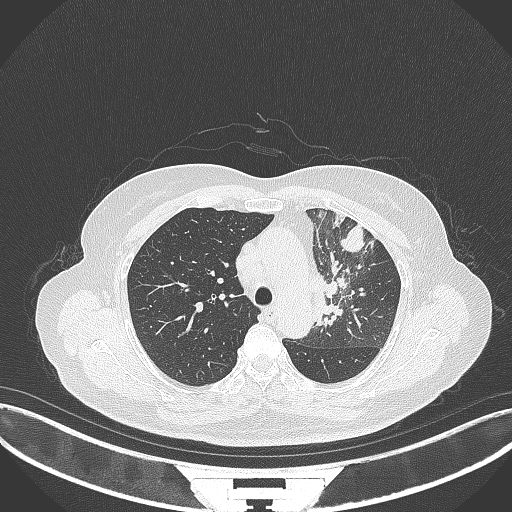
Chest CT, one axial slice. Slice 243 of 382 in the series (ordered by position). Reconstruction kernel B70f. 120 kVp. Lung window (W 1500 / L -600 HU). 1 mm slice thickness. 512 × 512 image matrix. Female patient, age 64 years. From the clinical record (not read from this slice): clinical TNM (as recorded): T2a N2 M0.
Structures marked on this image (bounding box drawn by a radiologist):
- lung tumour (recorded histology: adenocarcinoma): bounding box [x1, y1, x2, y2] px = [311, 257, 352, 331]
- lung tumour (recorded histology: adenocarcinoma): [340, 221, 373, 253]